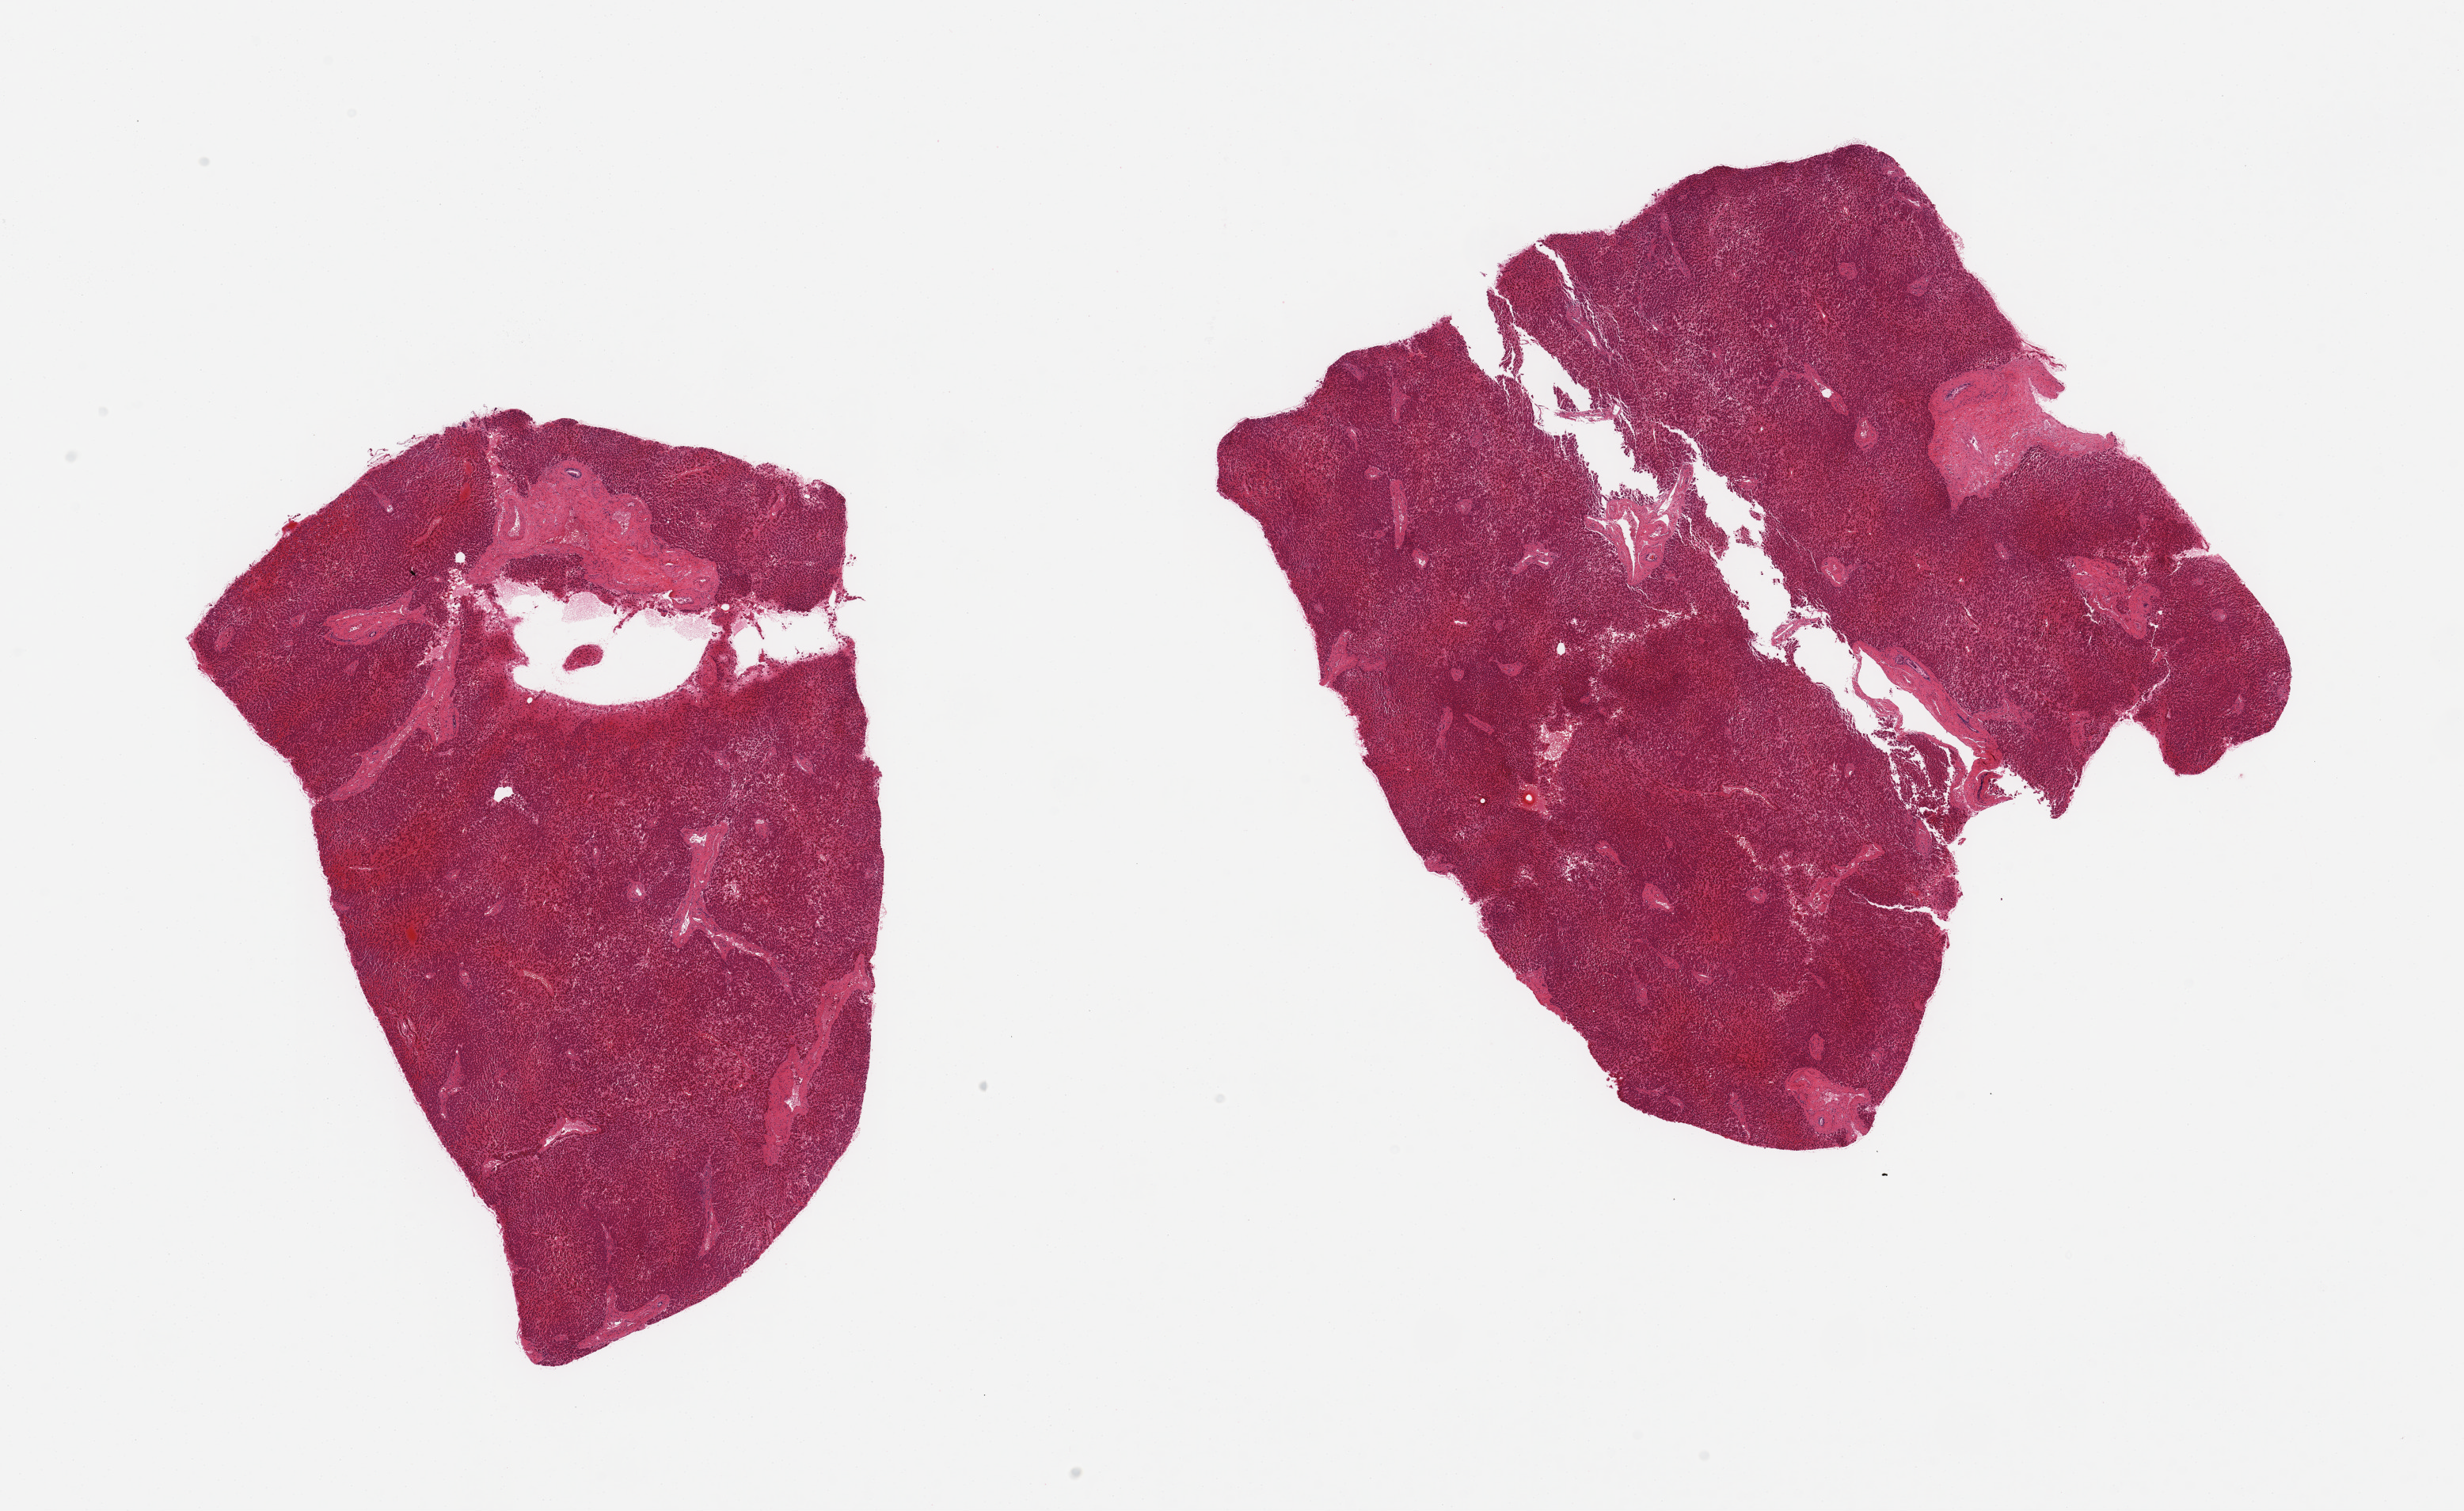
Digitized H&E-stained section — whole scanned area (about 24.6 x 15.1 mm, acquisition: 20x scan) shown as a low-resolution overview. PAXgene-fixed paraffin-embedded (PFPE) section. Sampled site (target tissue): liver. Tissue donor sample. Male donor.
• pathologist's review note for this sample: 2 pieces; congestion